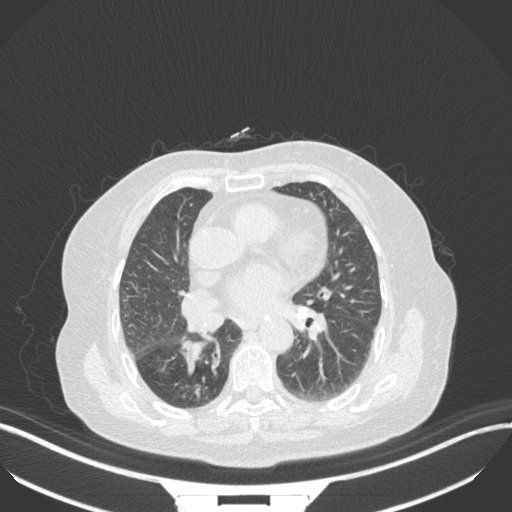
Chest CT, one axial slice. Position 153 of 329 along the scan axis. Reconstruction kernel B31f. 120 kVp. Lung window (W 1500 / L -600 HU). 1 mm slice thickness. 512 × 512 image matrix, field of view 400 × 400 mm. Patient: female, 75 years. From the clinical record (not read from this slice): clinical TNM (as recorded): T1b N0 M1a; histopathological grade: G1.
Structures marked on this image (rectangle marked by the reading radiologist):
- lung tumour (recorded histology: squamous cell carcinoma): box from (x=181, y=336) to (x=204, y=373) px